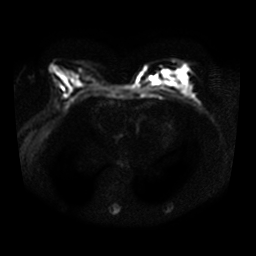
Breast MRI, one axial slice. Slice 14 of 32 in the series (ordered by position). Diffusion-weighted series; image 2 of 4 stored at this slice position (different b-values; order by instance number). 3 T. 5 mm slice thickness. 256 × 256 image matrix, field of view 340 × 340 mm. Female patient.
Annotated regions visible in this slice (manually delineated by an expert):
- tumour on diffusion-weighted imaging: bounding box (x1, y1, x2, y2) in pixels: (150, 72, 181, 85)